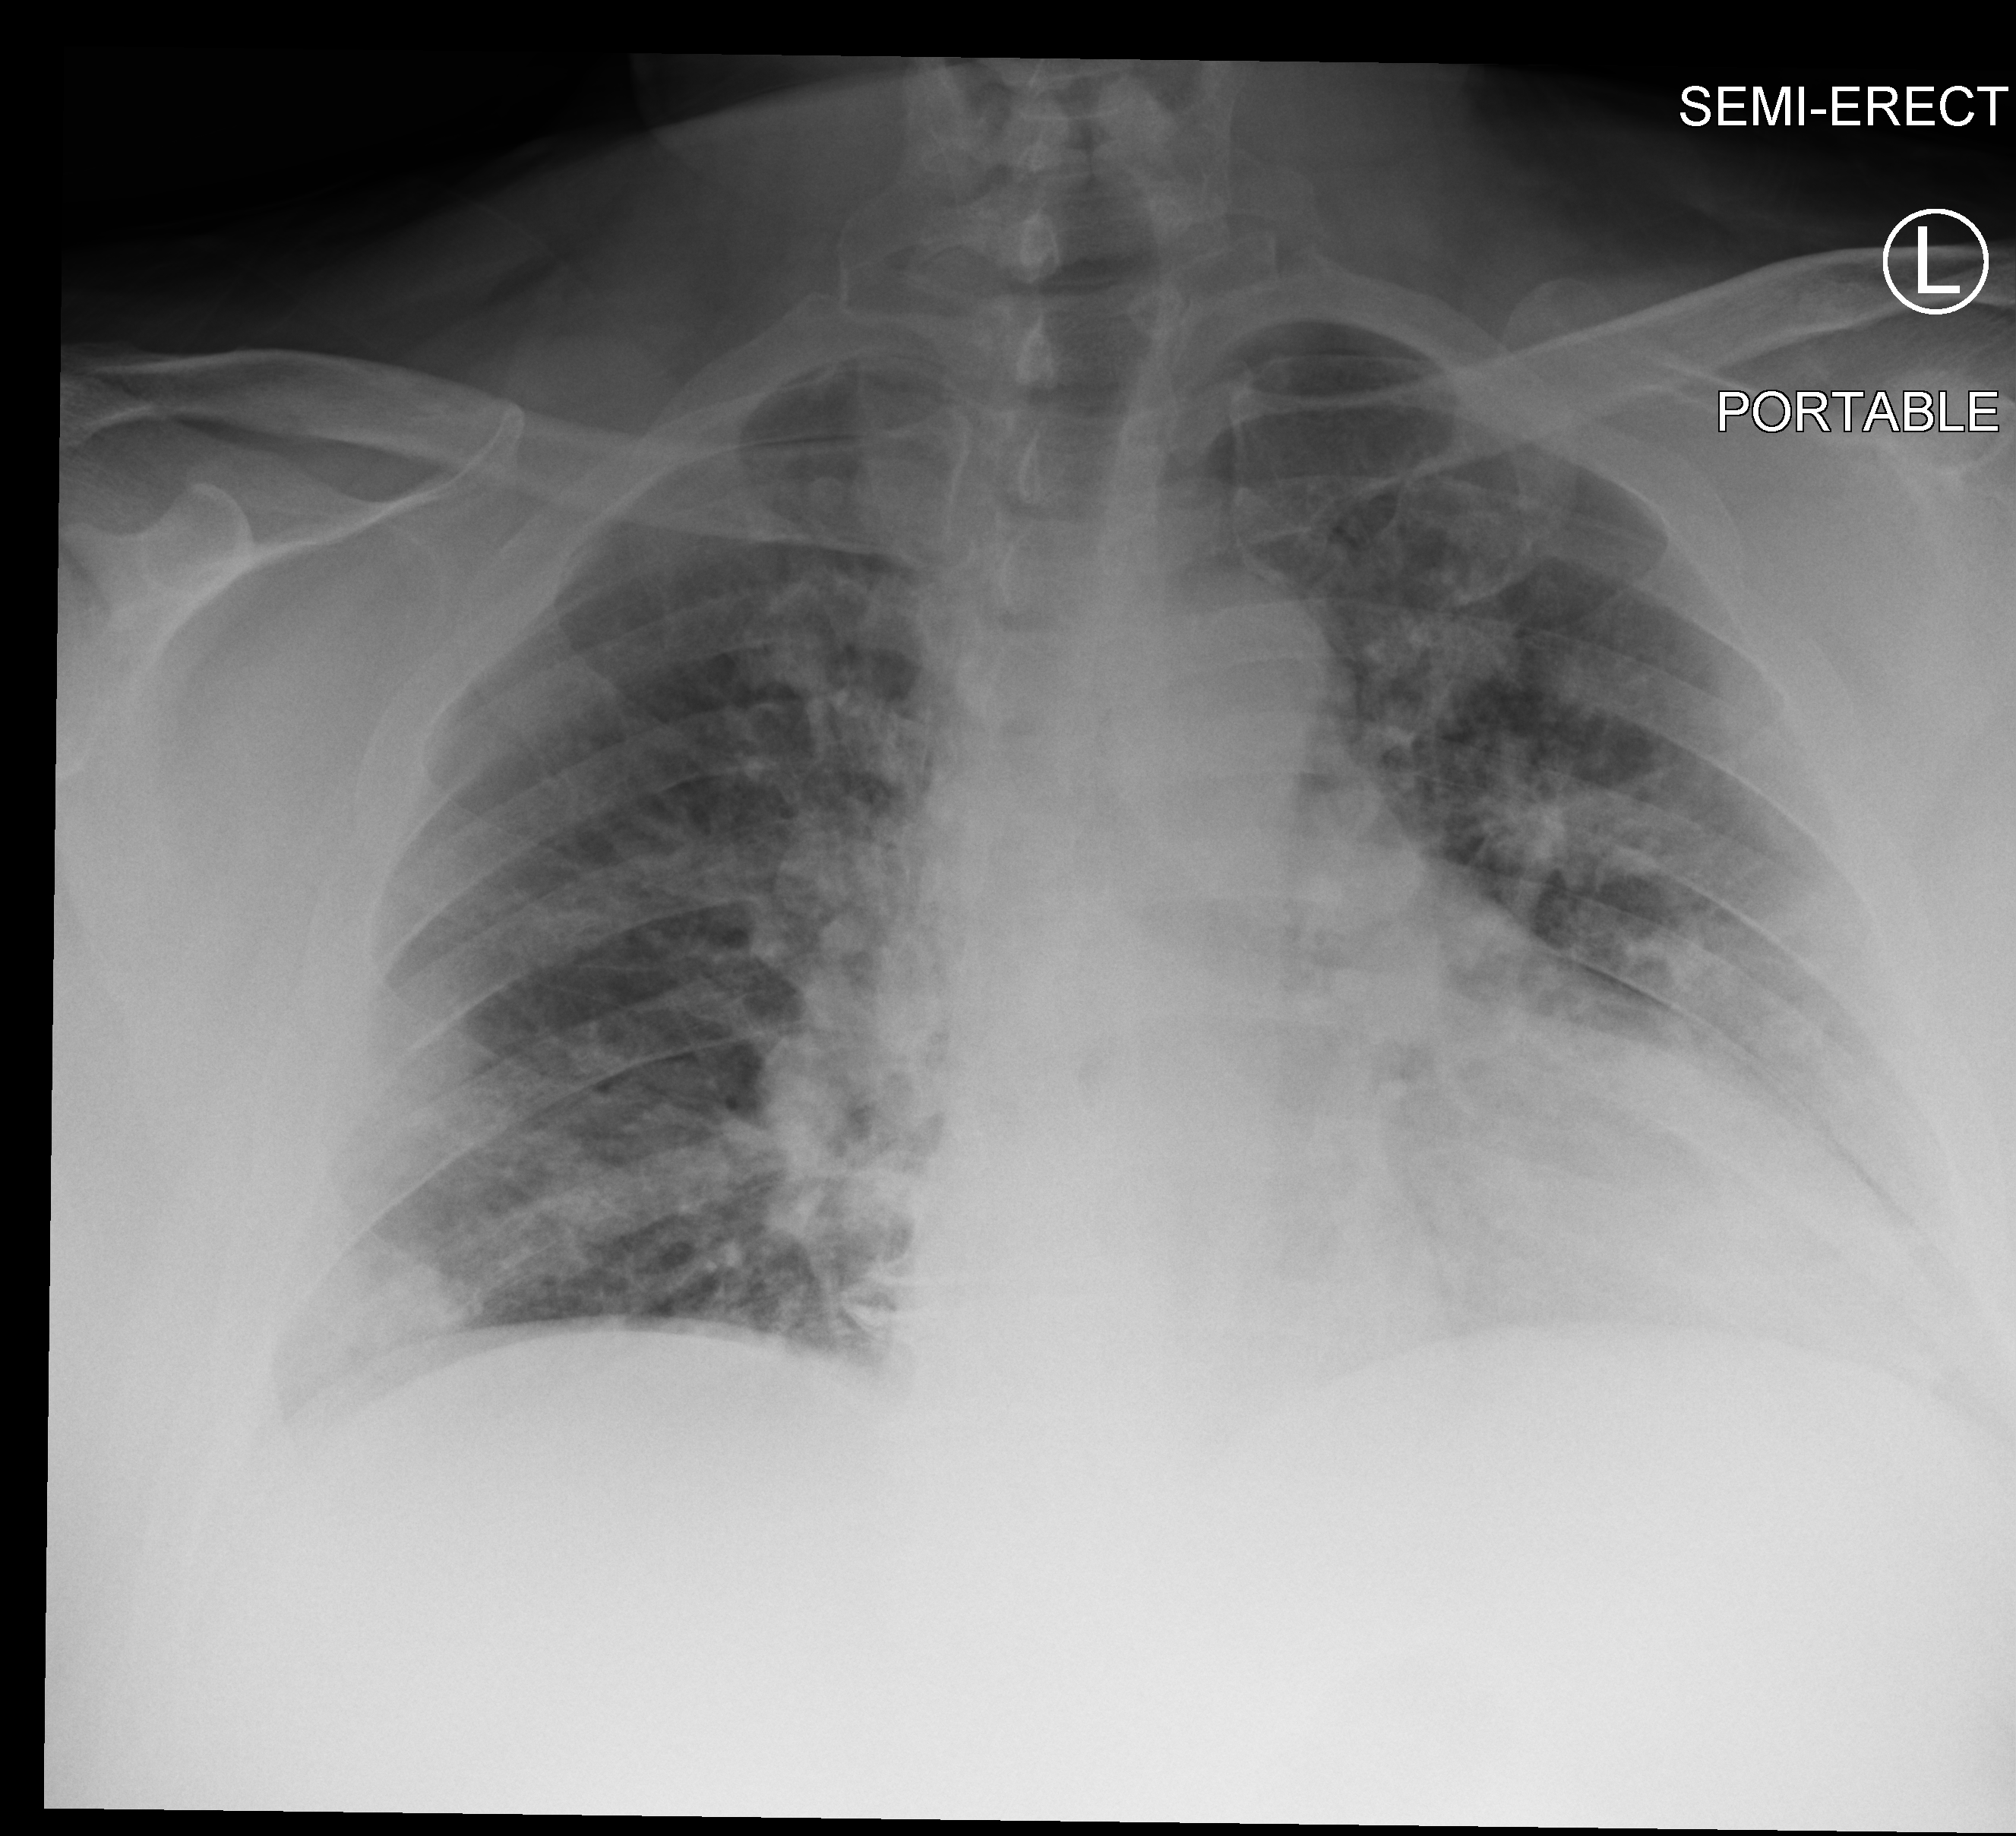
Chest X-ray (portable). Patient hospitalised with COVID-19; male, aged 18–59 years.
Admission-level facts for this patient (not findings on this image; timing relative to this image not recorded): hypertension (admission record): no; mechanically ventilated during this hospital stay: no; other chronic lung disease (admission record): no.